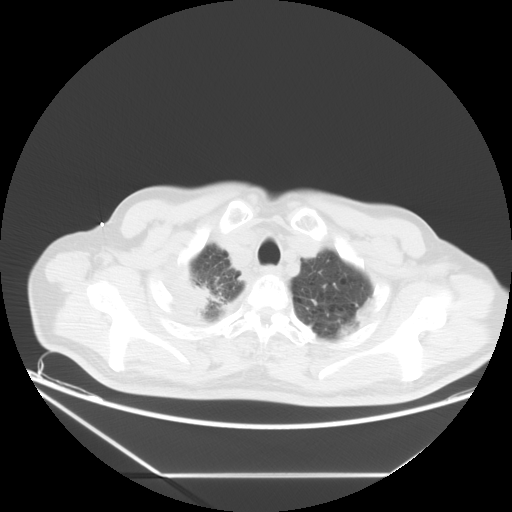
Chest CT, one axial slice; position 18 of 20 along the scan axis; reconstruction kernel STANDARD; lung window (W 1500 / L -600 HU); 5 mm slice thickness; 512 × 512 image matrix. Patient: male, 75 years. Case-level facts recorded for this patient, not image findings: clinical TNM (as recorded): T1c N1 M1.
Structures marked on this image (rectangle marked by the reading radiologist):
- lung tumour (recorded histology: adenocarcinoma): box from (x=189, y=285) to (x=215, y=312) px